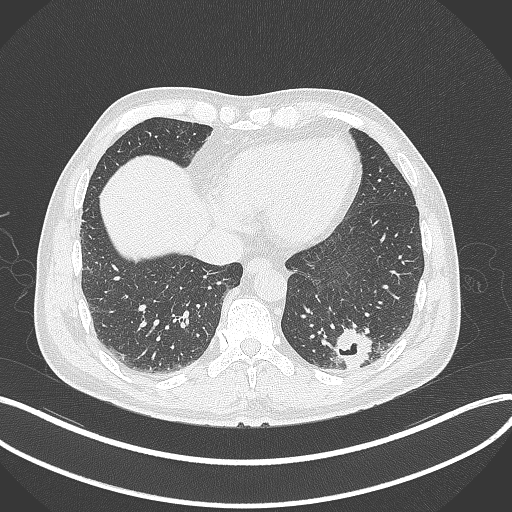
Chest CT, one axial slice; slice 75 of 300 in the series (ordered by position); 120 kVp; lung window (W 1500 / L -600 HU); 1 mm slice thickness; 512 × 512 image matrix, field of view 400 × 400 mm. Male patient, age 54 years. Case-level facts recorded for this patient, not image findings: clinical TNM (as recorded): T1c N0 M1; histopathological grade: G3.
Outlined on this slice (bounding box drawn by a radiologist):
- lung tumour (recorded histology: adenocarcinoma): bounding box [x1, y1, x2, y2] px = [333, 327, 370, 370]